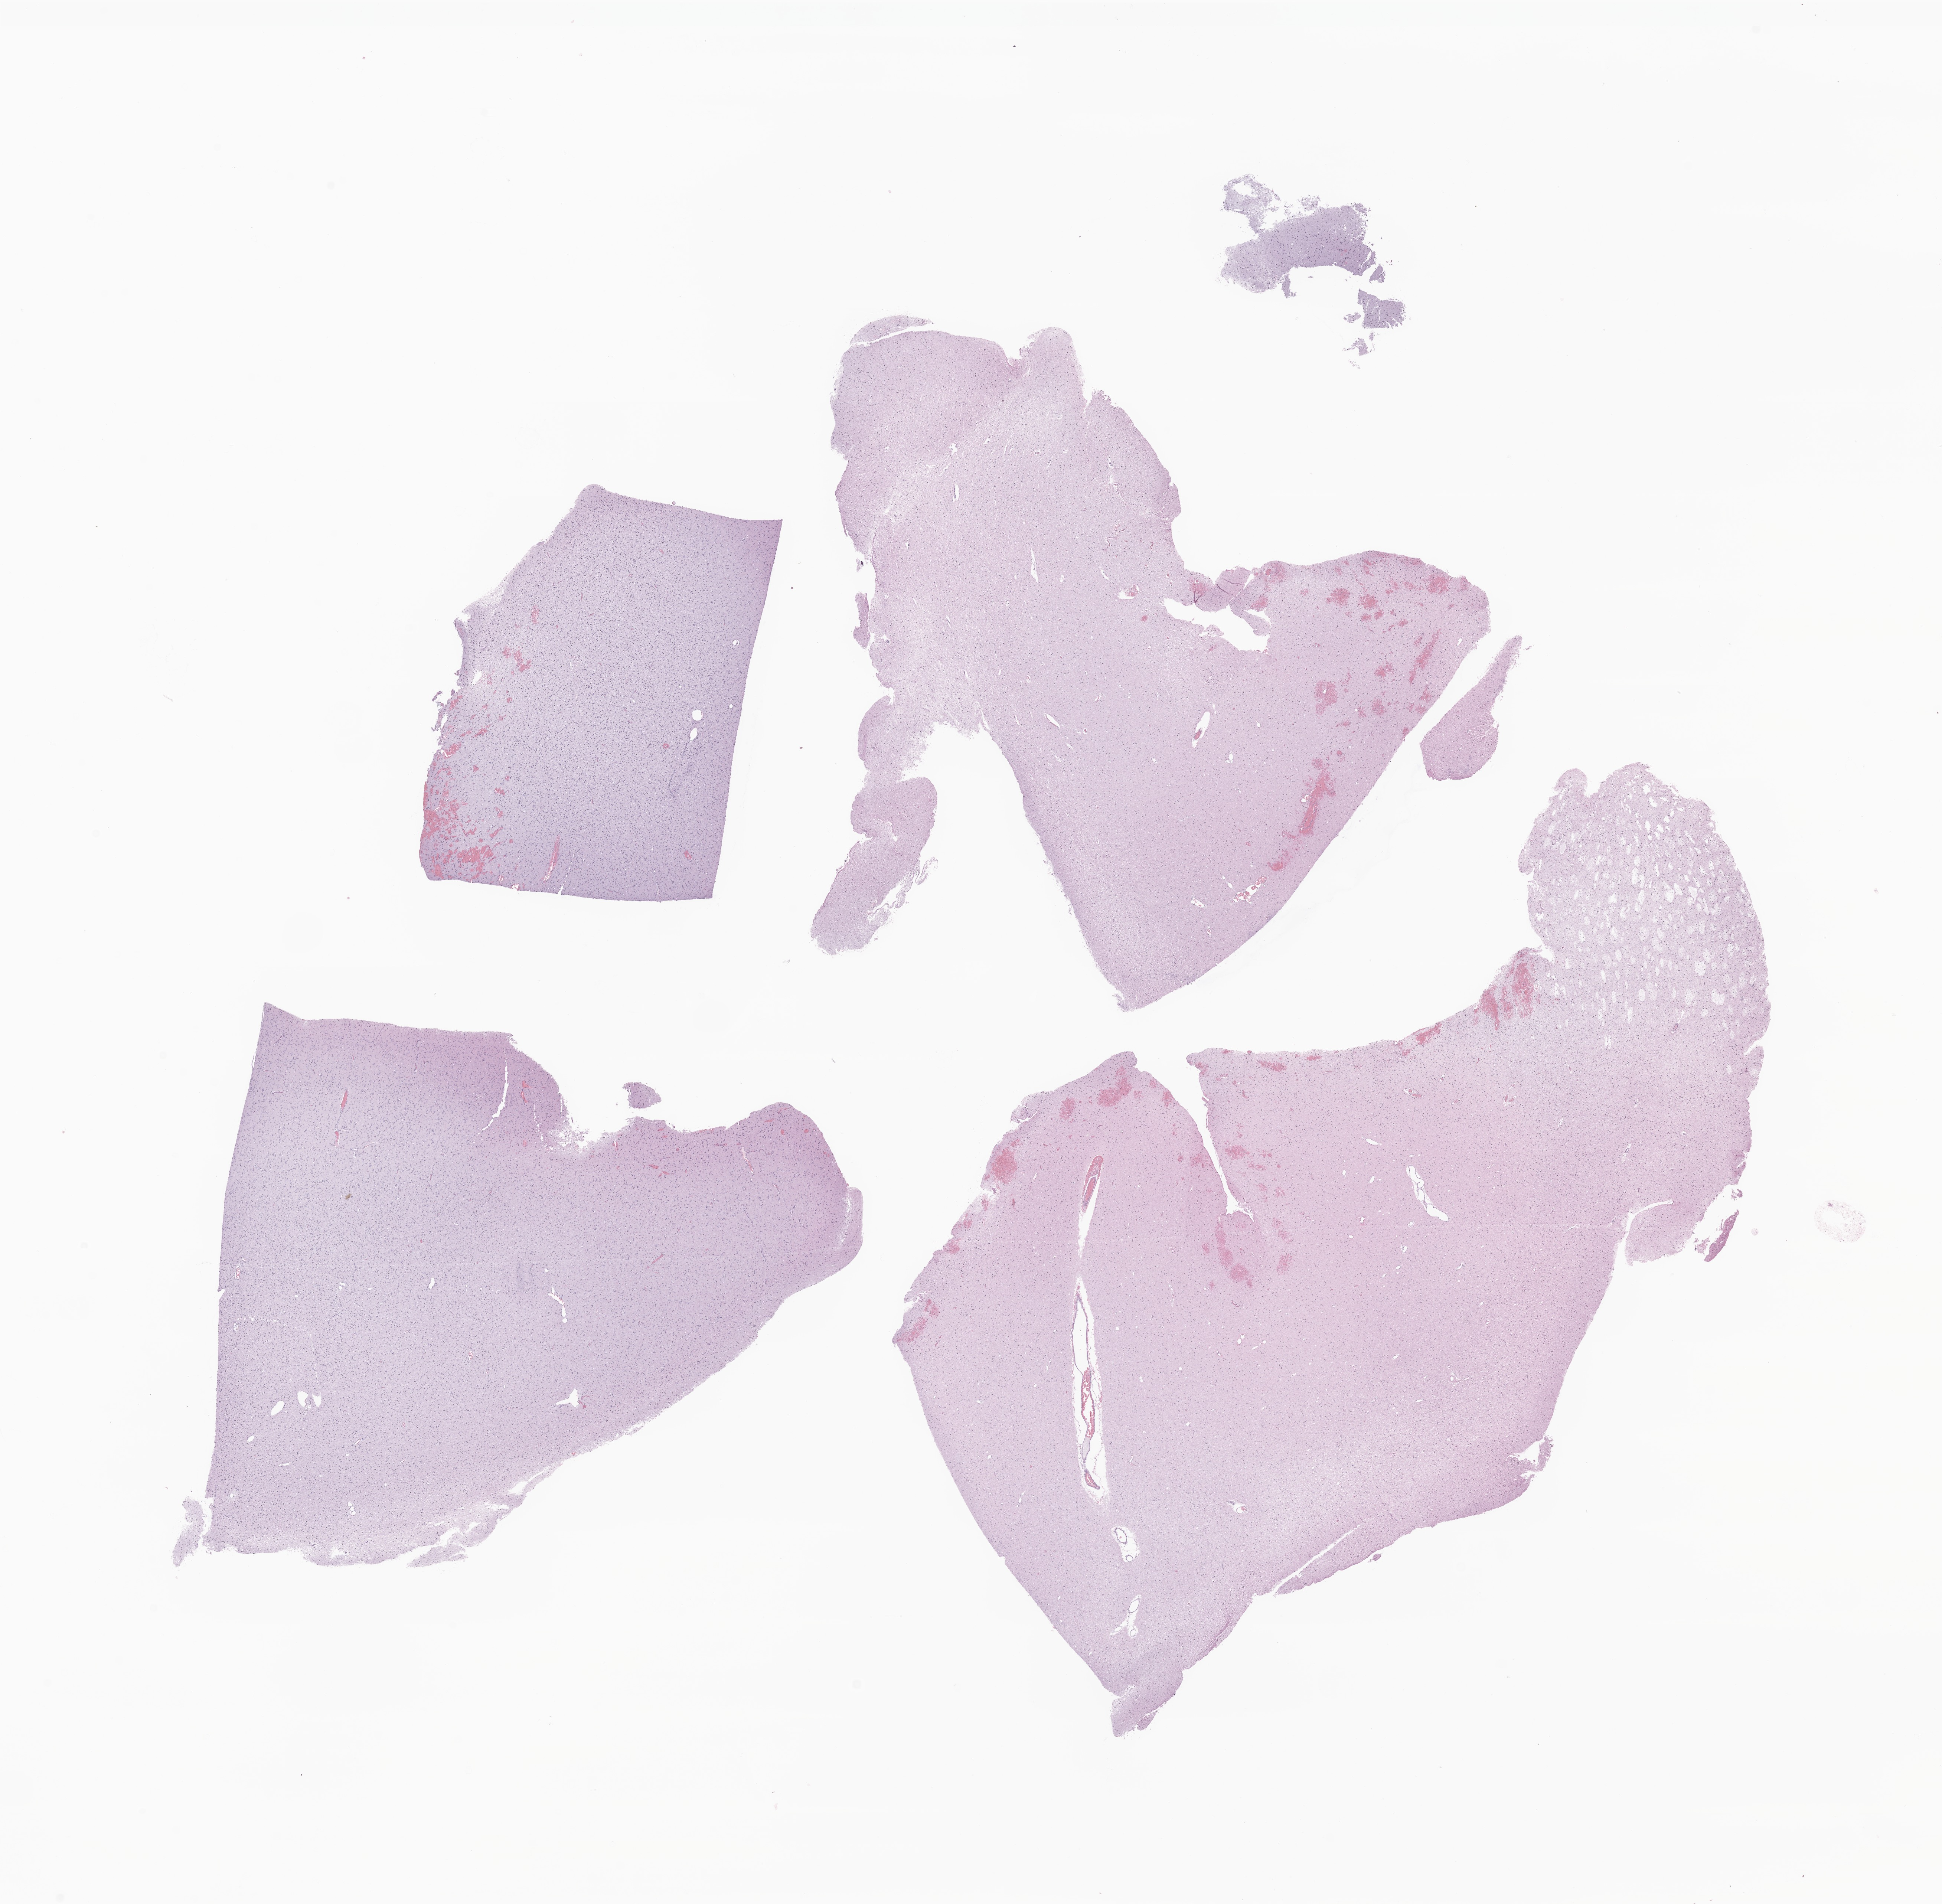
Whole-slide image, haematoxylin and eosin stain of tumor tissue from the frontal lobe — a low-resolution overview of the entire scanned area, about 22.1 x 21.6 mm. Formalin-fixed, paraffin-embedded (FFPE) tissue. Patient female; age 220 months (18 years 4 months).
* recorded diagnosis: Oligoastrocytoma, NOS